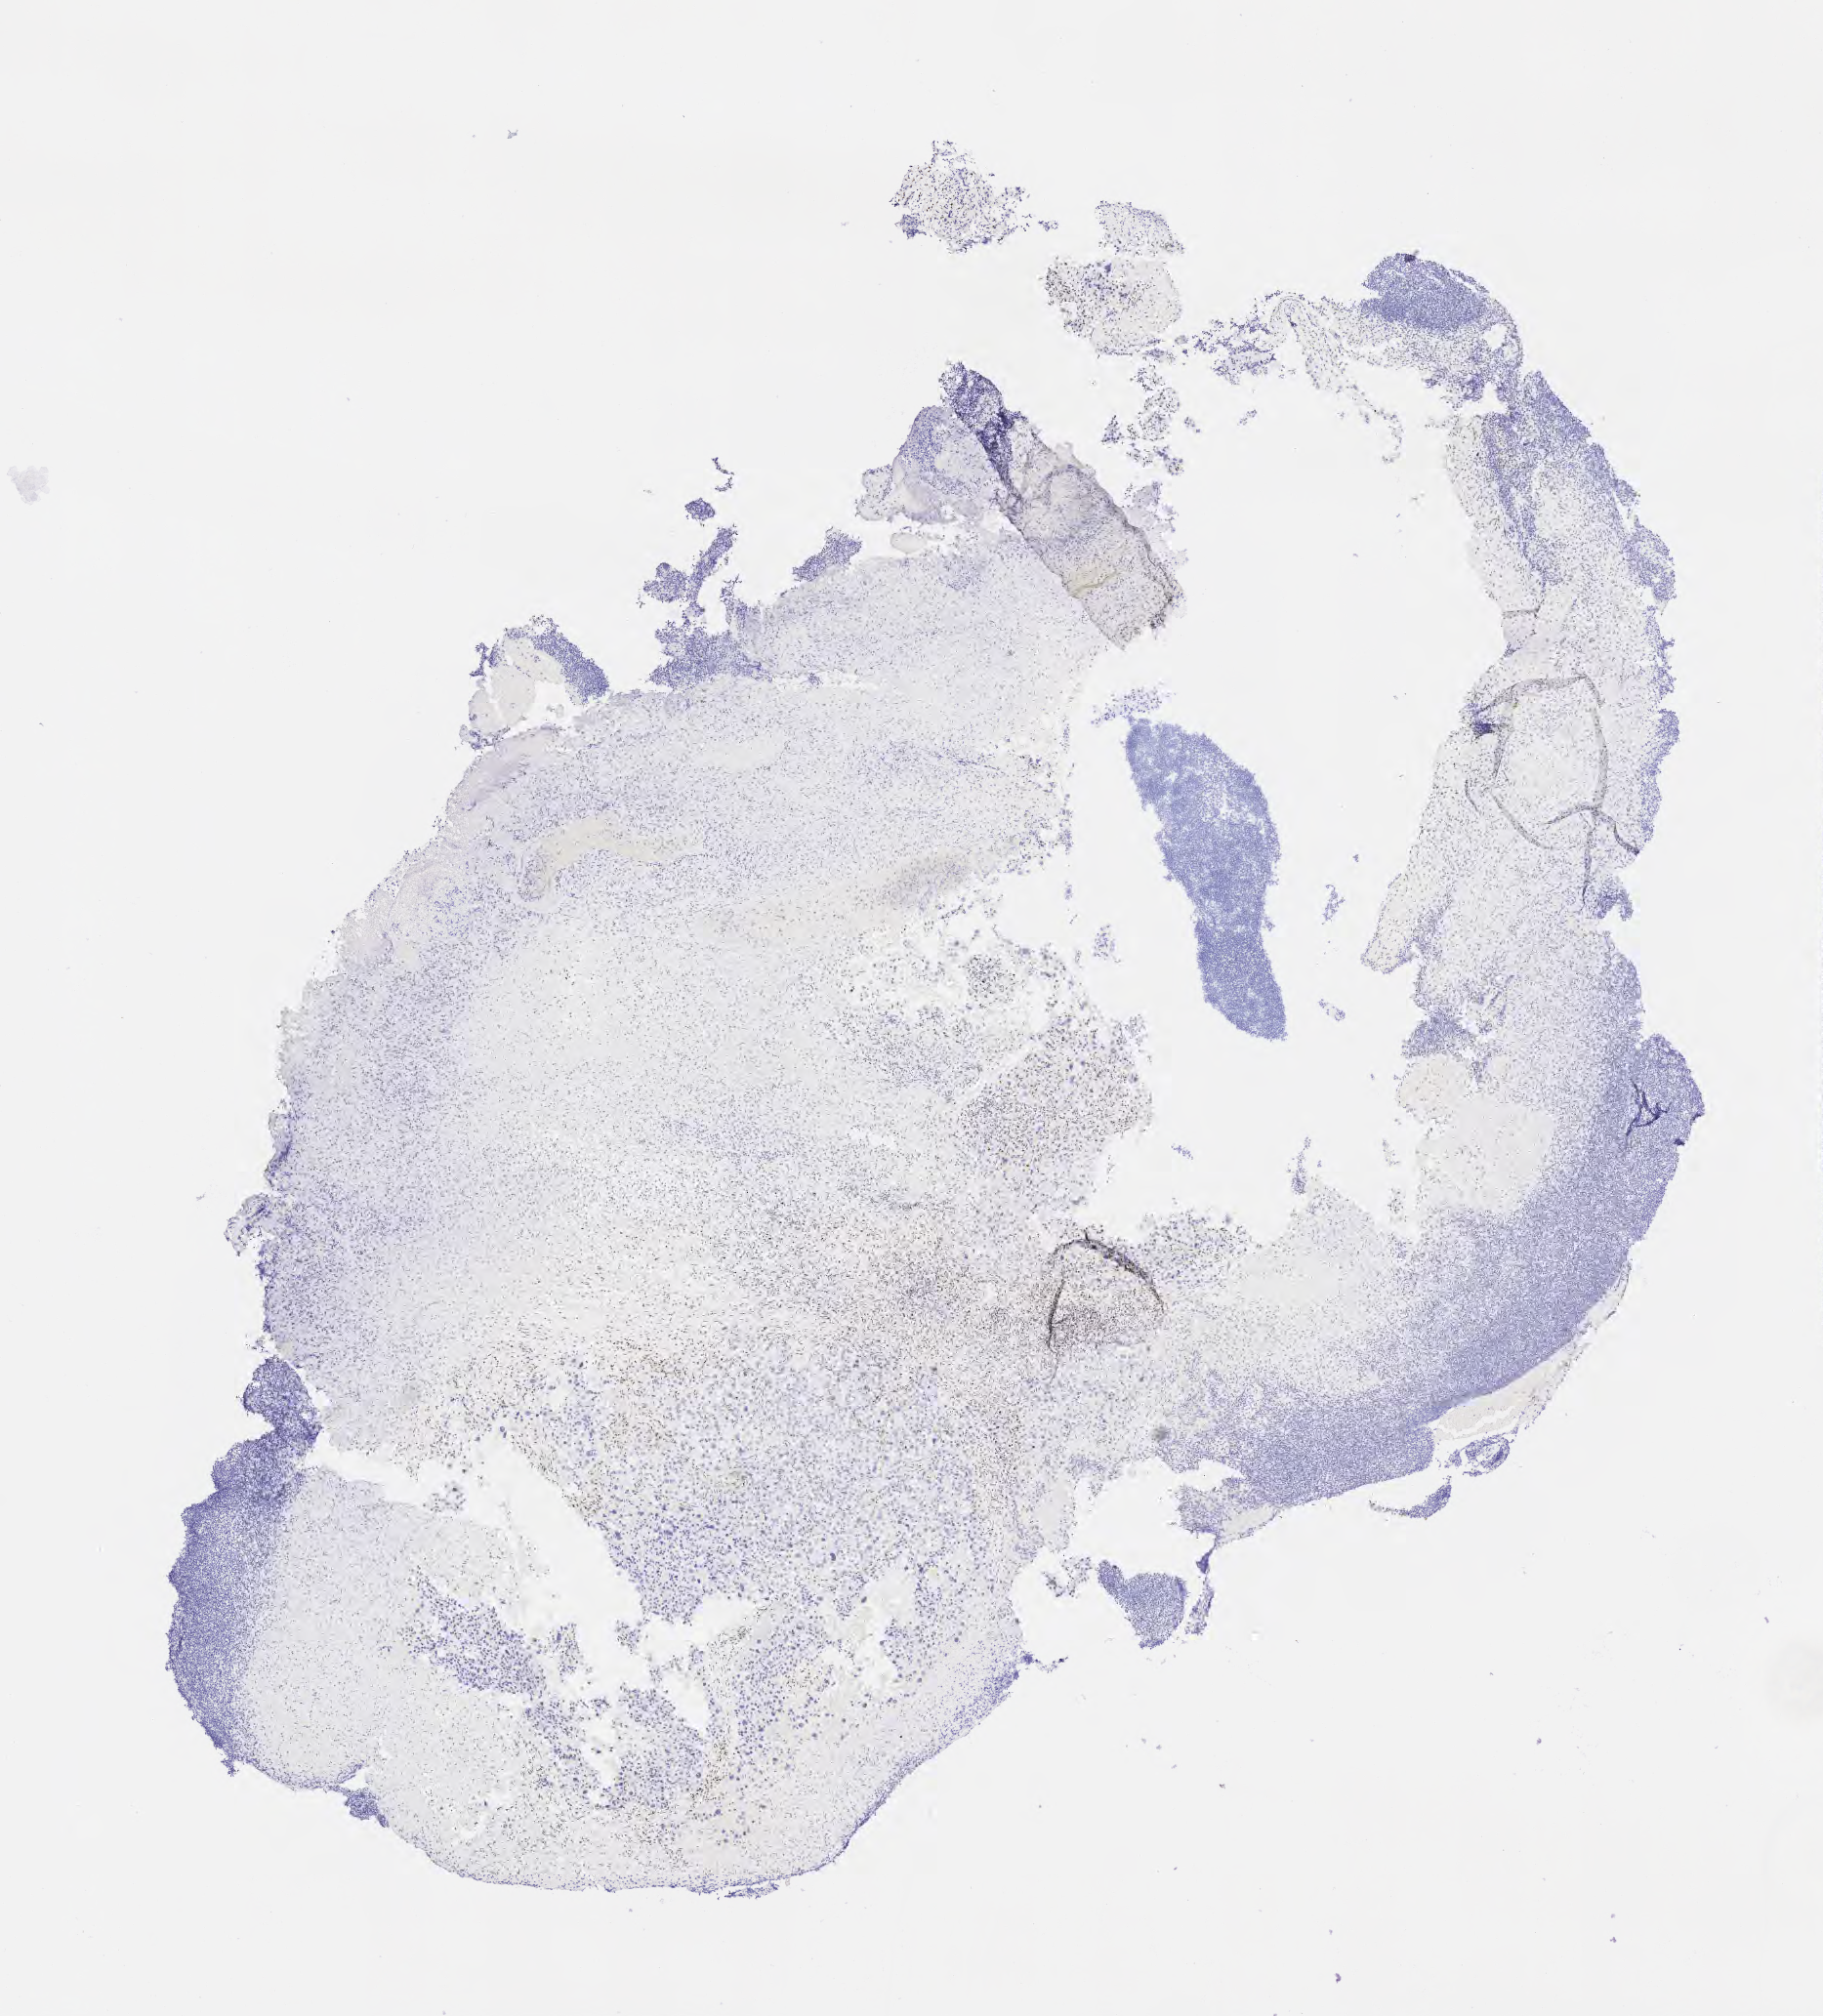
Whole-slide image, immunohistochemical stain for p53, a low-resolution overview of the entire scanned area, about 7.5 x 8.3 mm, specimen: tumor tissue, anatomic site: cervix. Patient: female, 62 years old.
Diagnosis: Squamous cell carcinoma, large cell, nonkeratinizing, NOS.